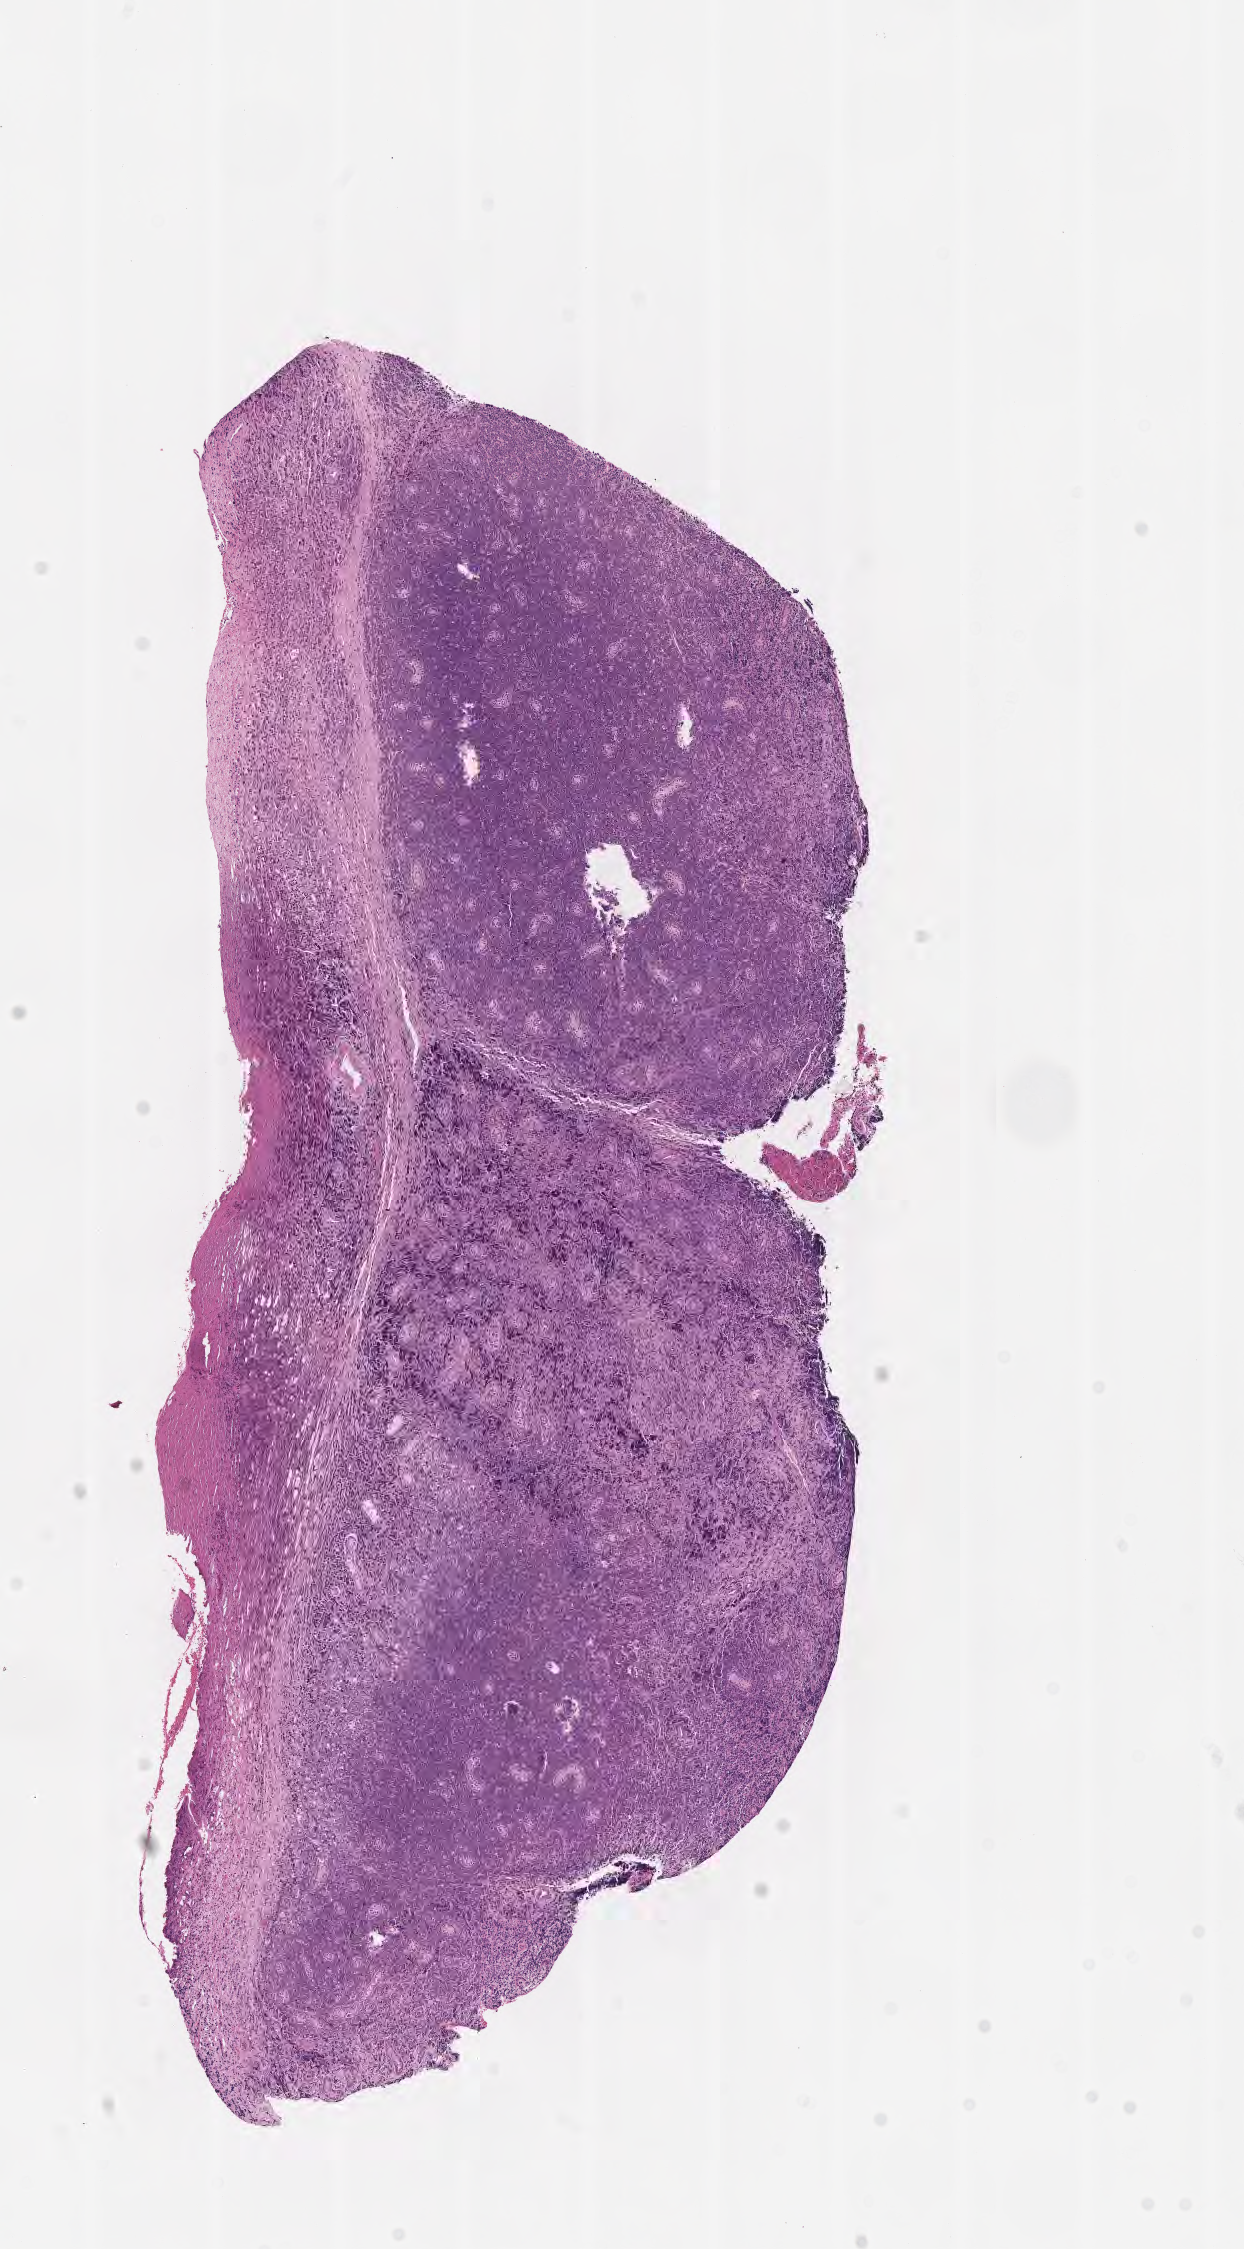
Whole-slide image, H&E stain, low-resolution overview of the scanned area, about 5.0 x 9.1 mm. Specimen: tumor tissue. Site: testis. Patient: male, age at initial diagnosis 8 years.
* histologic diagnosis: Burkitt lymphoma, NOS